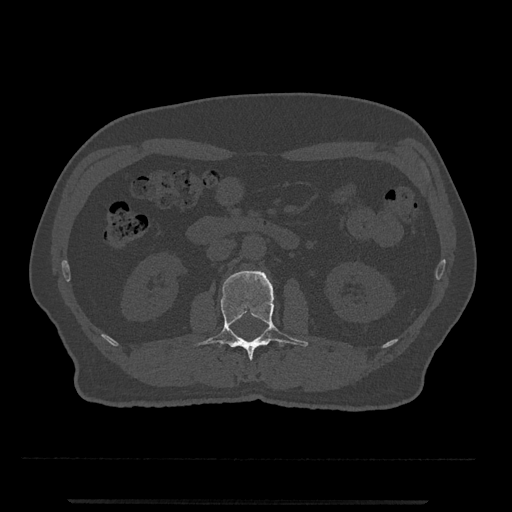
CT including the spine, one axial slice; slice 267 of 797 in the series (ordered by position); reconstruction kernel Br40s/3; bone window (W 1800 / L 400 HU); 0.5 mm slice thickness; 512 × 512 image matrix, field of view 419 × 419 mm. Patient: male, 63 years. Case-level facts recorded for this patient, not image findings: primary cancer: prostate.
Outlined on this slice (semi-automatic segmentation, software-assisted and operator-edited):
- L2 vertebra: bounding box (x1, y1, x2, y2) in pixels: (195, 270, 308, 361)